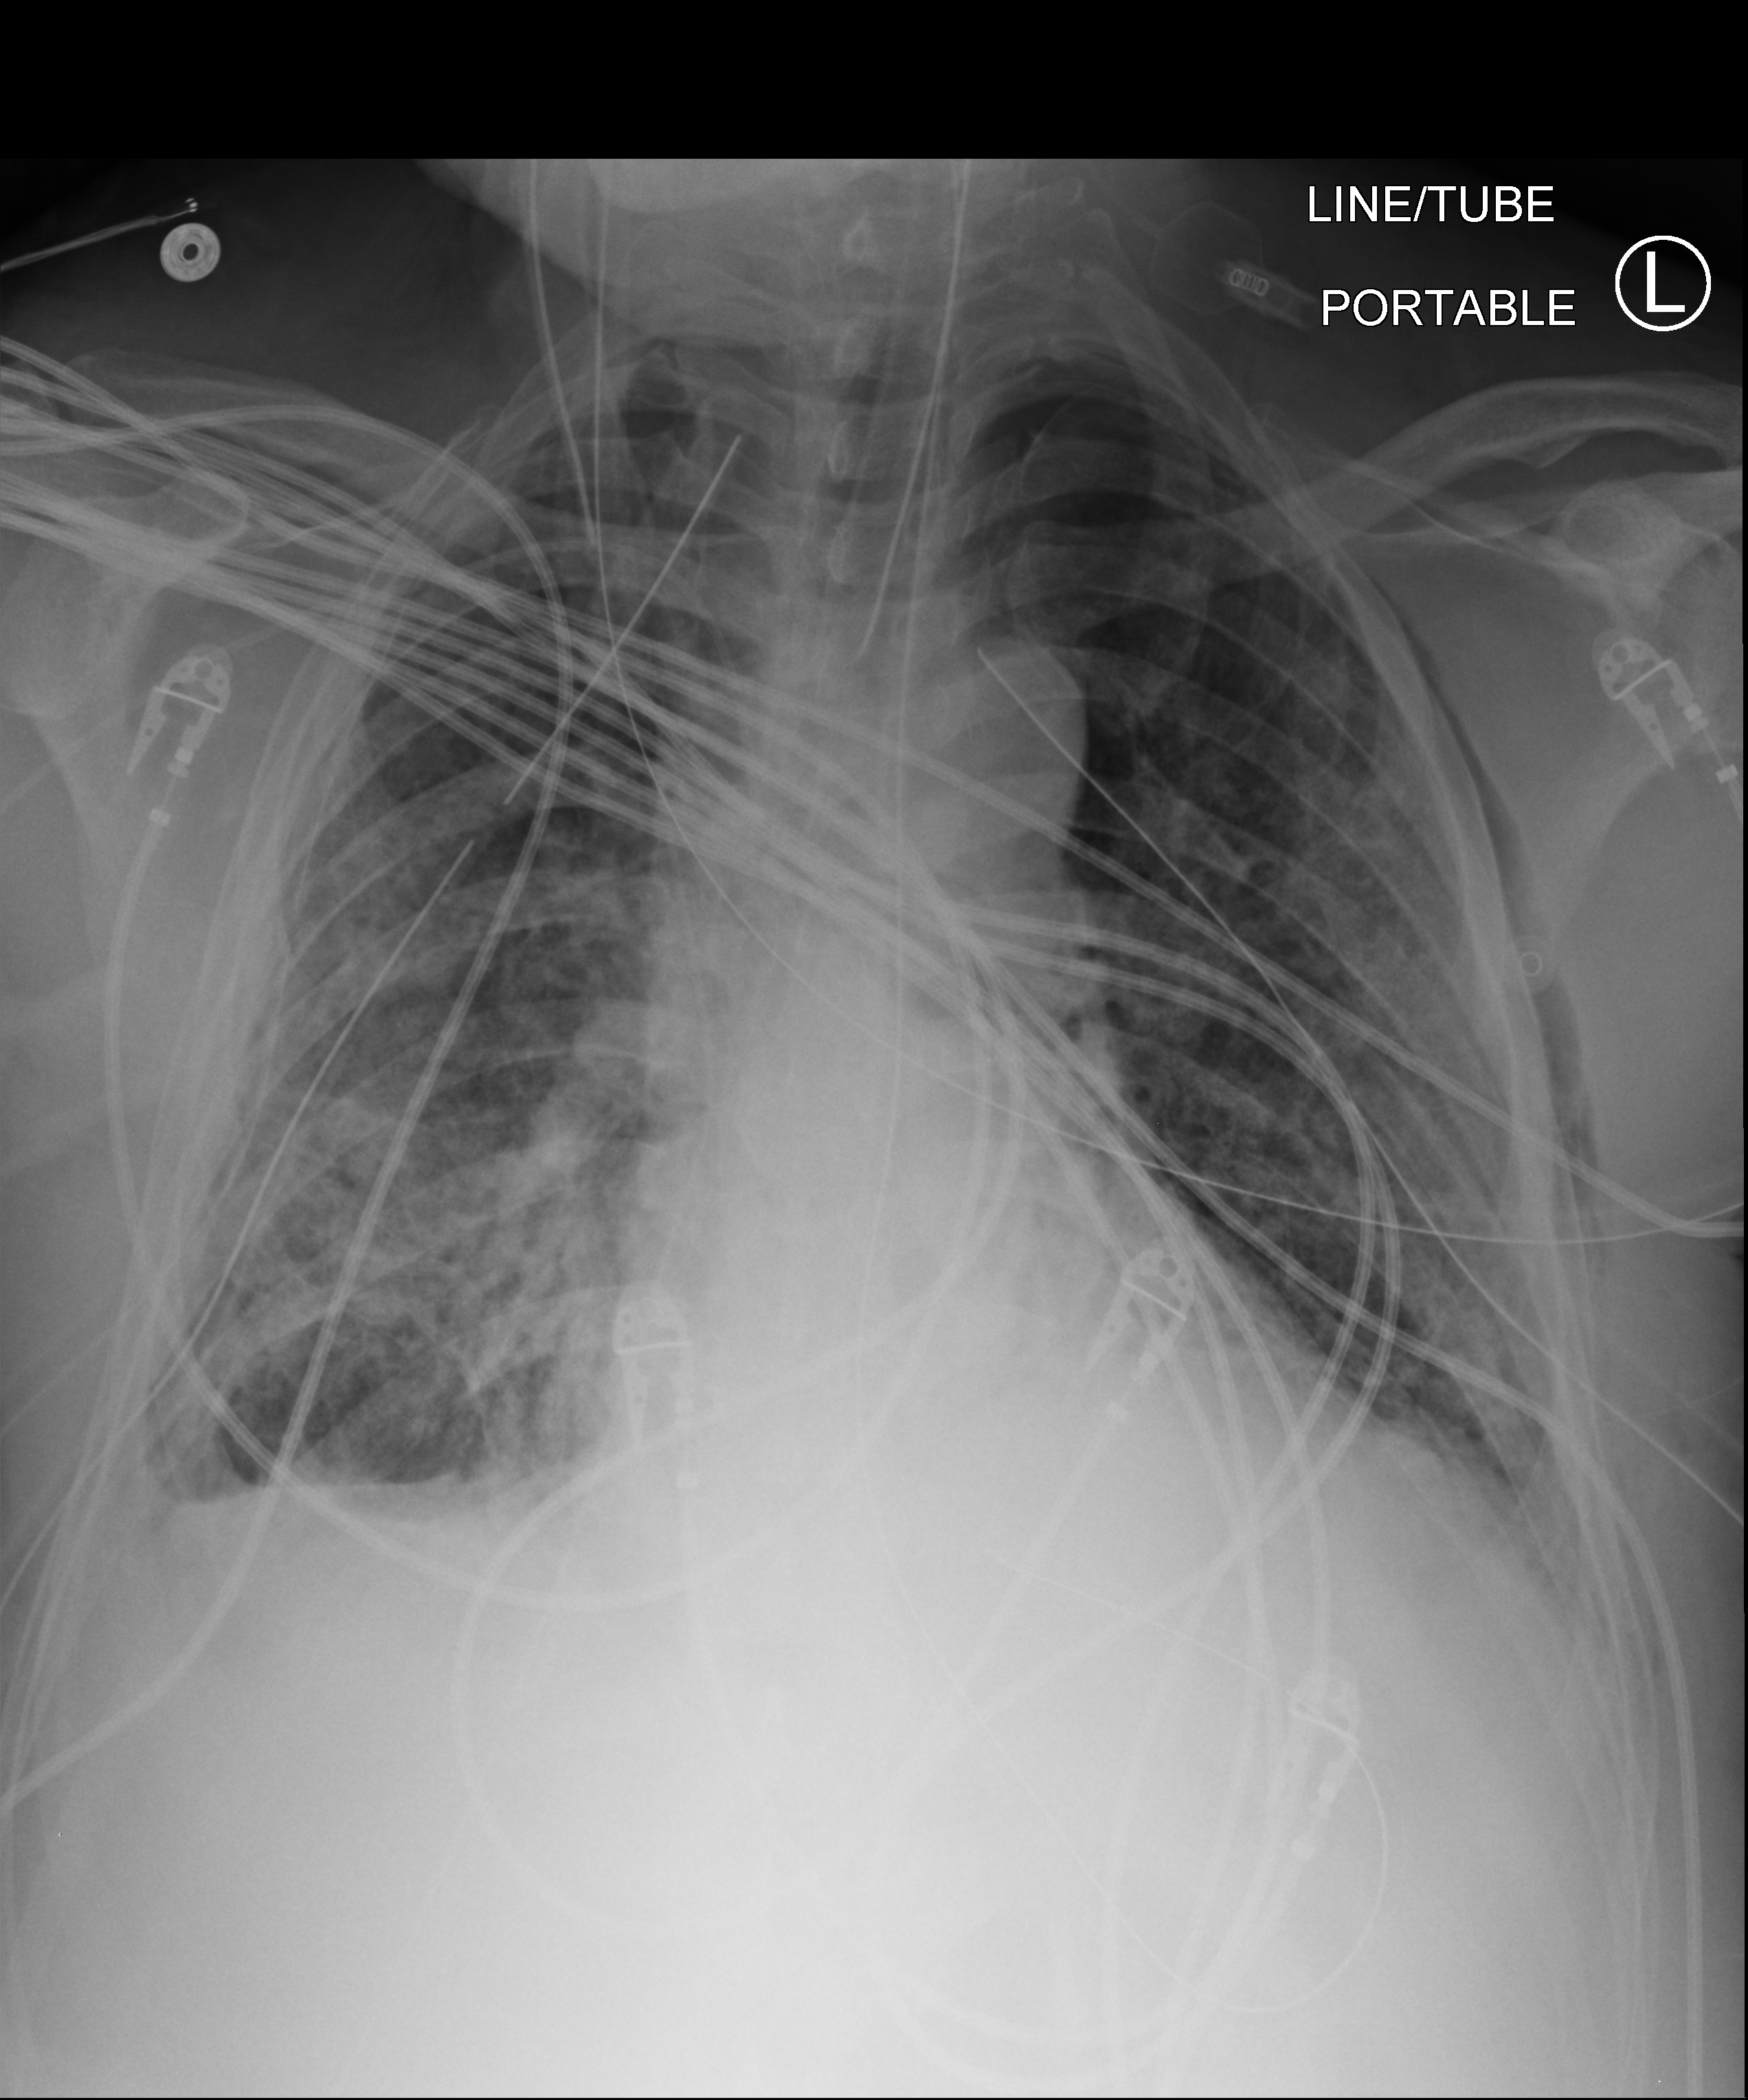
Chest X-ray (portable); anteroposterior (AP) projection. Male patient hospitalised with COVID-19, age 60–74 years.
Admission-level facts for this patient (not findings on this image; timing relative to this image not recorded):
- admitted to intensive care during this hospital stay: yes